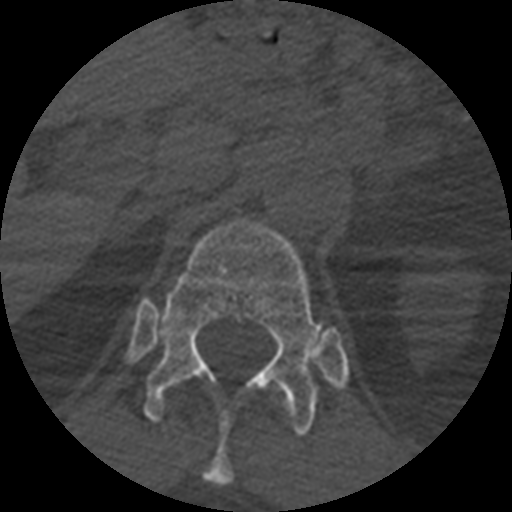
CT including the spine, one axial slice; position 391 of 399 along the scan axis; reconstruction kernel STANDARD; 120 kVp; bone window (W 1800 / L 400 HU); 1.25 mm slice thickness; 512 × 512 image matrix. Patient age 71 years. Case-level facts recorded for this patient, not image findings: primary cancer: prostate.
Annotated regions visible in this slice (semi-automatically segmented with operator editing):
- T11 vertebra: bounding box [x1, y1, x2, y2] px = [205, 399, 286, 486]
- T12 vertebra: [144, 217, 323, 434]